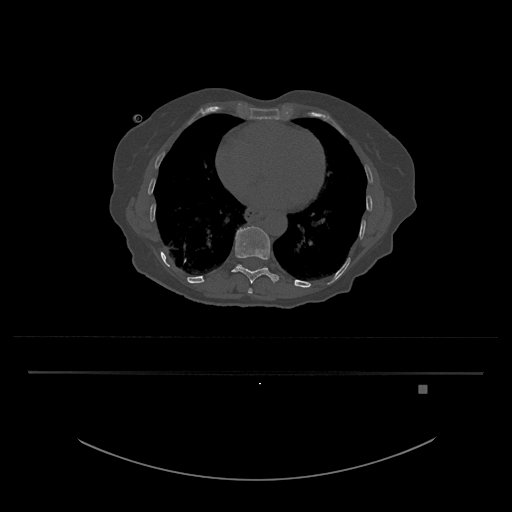
CT including the spine, one axial slice. Position 709 of 797 along the scan axis. Reconstruction kernel Br40s/3. 120 kVp. Bone window (W 1800 / L 400 HU). 0.5 mm slice thickness. 512 × 512 image matrix, field of view 500 × 500 mm. Female patient, age 57 years. Case-level facts recorded for this patient, not image findings: primary cancer: cervical.
Outlined on this slice (semi-automatically segmented with operator editing):
- T10 vertebra: bounding box [x1, y1, x2, y2] px = [232, 226, 279, 284]
- T9 vertebra: [248, 288, 253, 294]